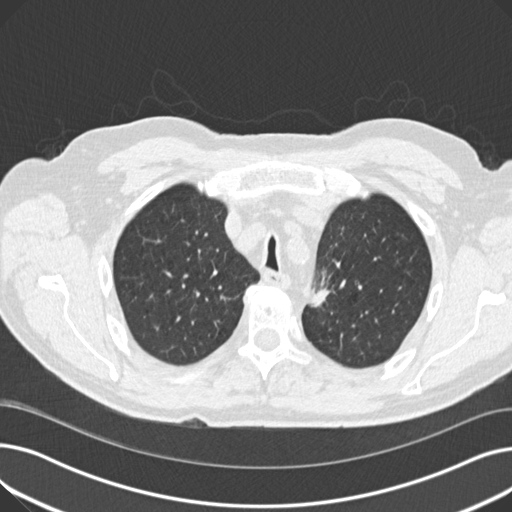
Low-dose screening chest CT, one axial slice; position 145 of 191 along the scan axis; reconstruction kernel B30f; 120 kVp; lung window (W 1500 / L -600 HU); 512 × 512 image matrix, field of view 370 × 370 mm.
Structures marked on this image (outlined manually by an expert reader):
- lesion 1 (tumor, upper lobe of left lung): box from (x=310, y=285) to (x=330, y=307) px